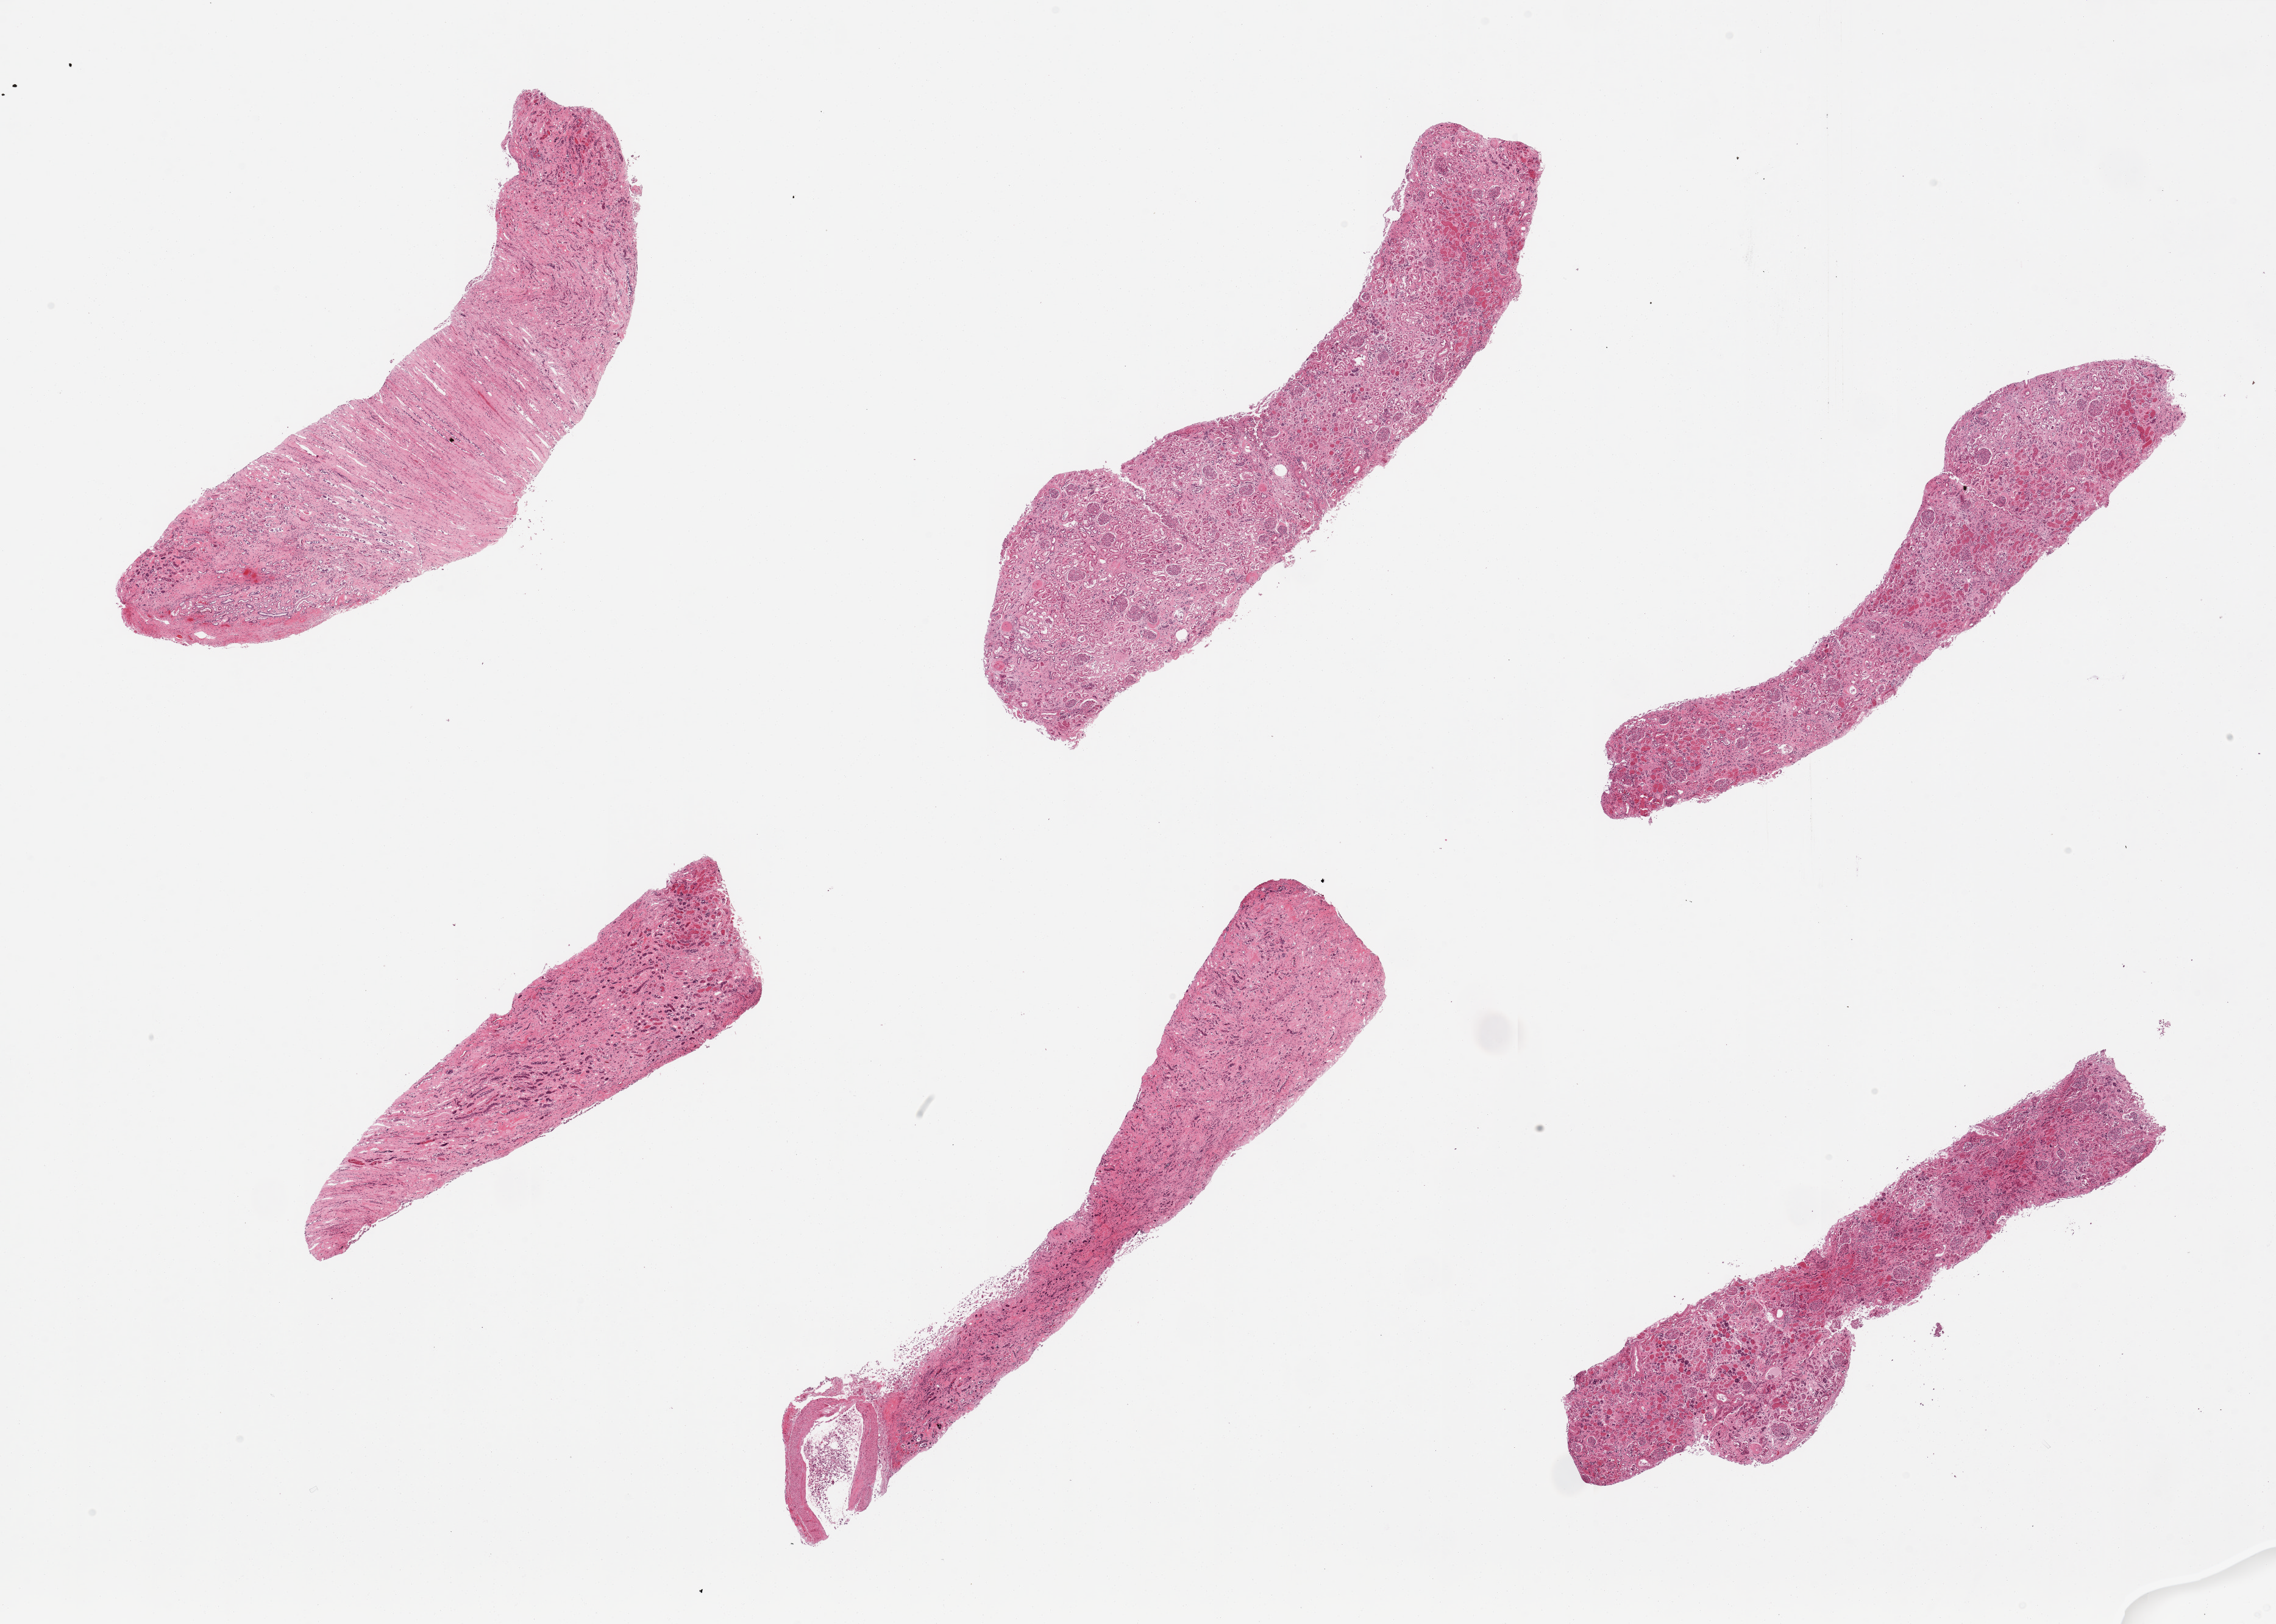
Whole-slide image, H&E stain, brightfield — low-resolution overview of the scanned area, about 29.5 x 21.1 mm (from a 20x scan). PAXgene-fixed, paraffin-embedded tissue. Target tissue: renal cortex. Donor tissue sample. Donor sex: male.
Reviewer comment on this tissue sample: 6 pieces, glomeruli present 4/6 sections; moderate tubular autolysis, interestitial fibrosis.